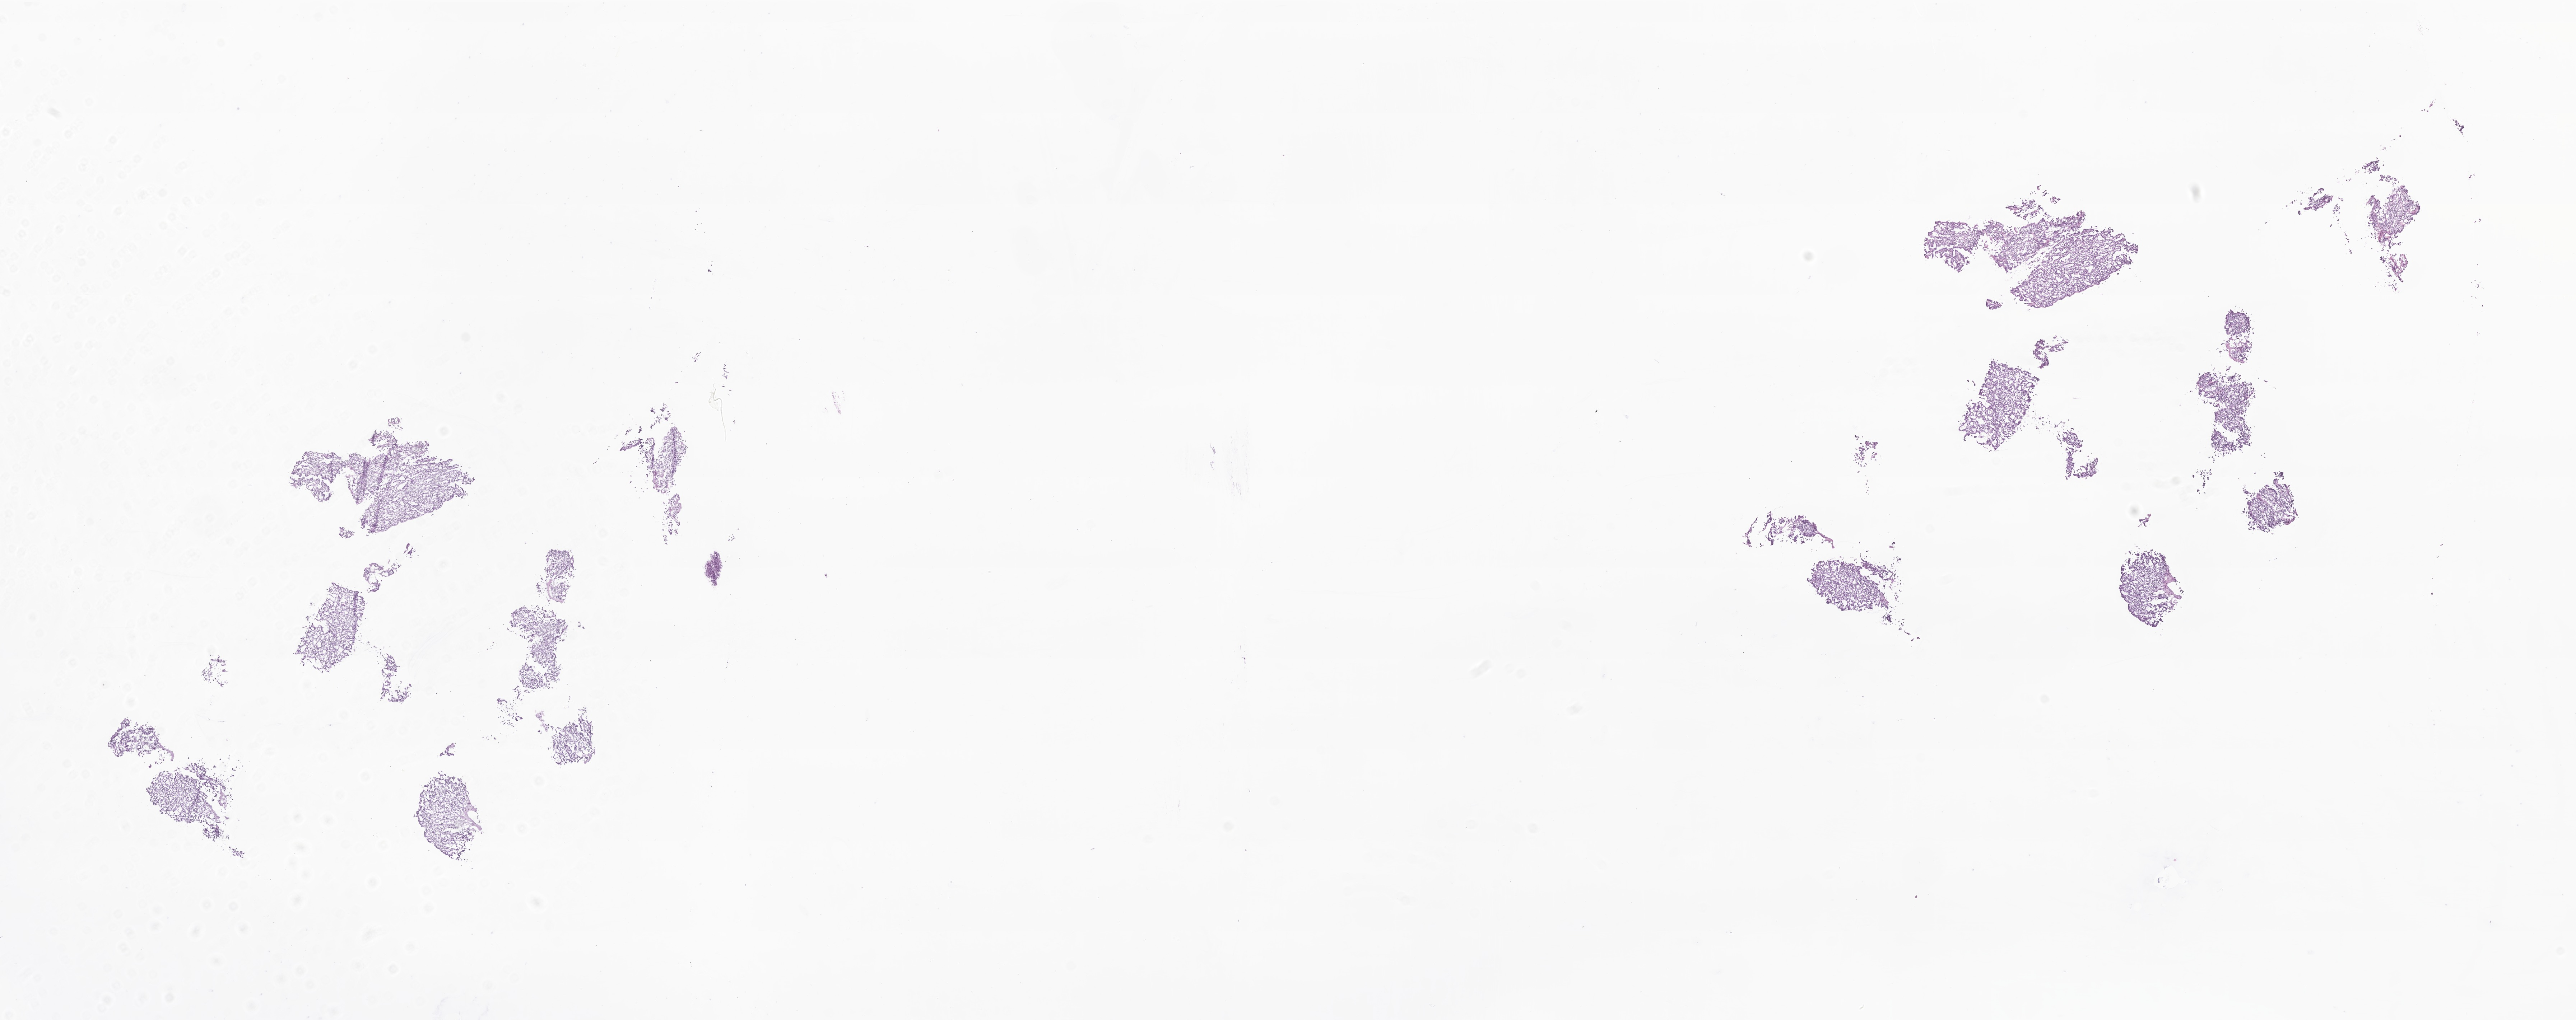
Whole-slide image, H&E stain of tumor tissue from the thyroid — a low-resolution overview of the entire scanned area, about 30.2 x 12.0 mm. Frozen section. Female patient, age 174 months (14 years 6 months).
Recorded diagnosis: Carcinoma, NOS.